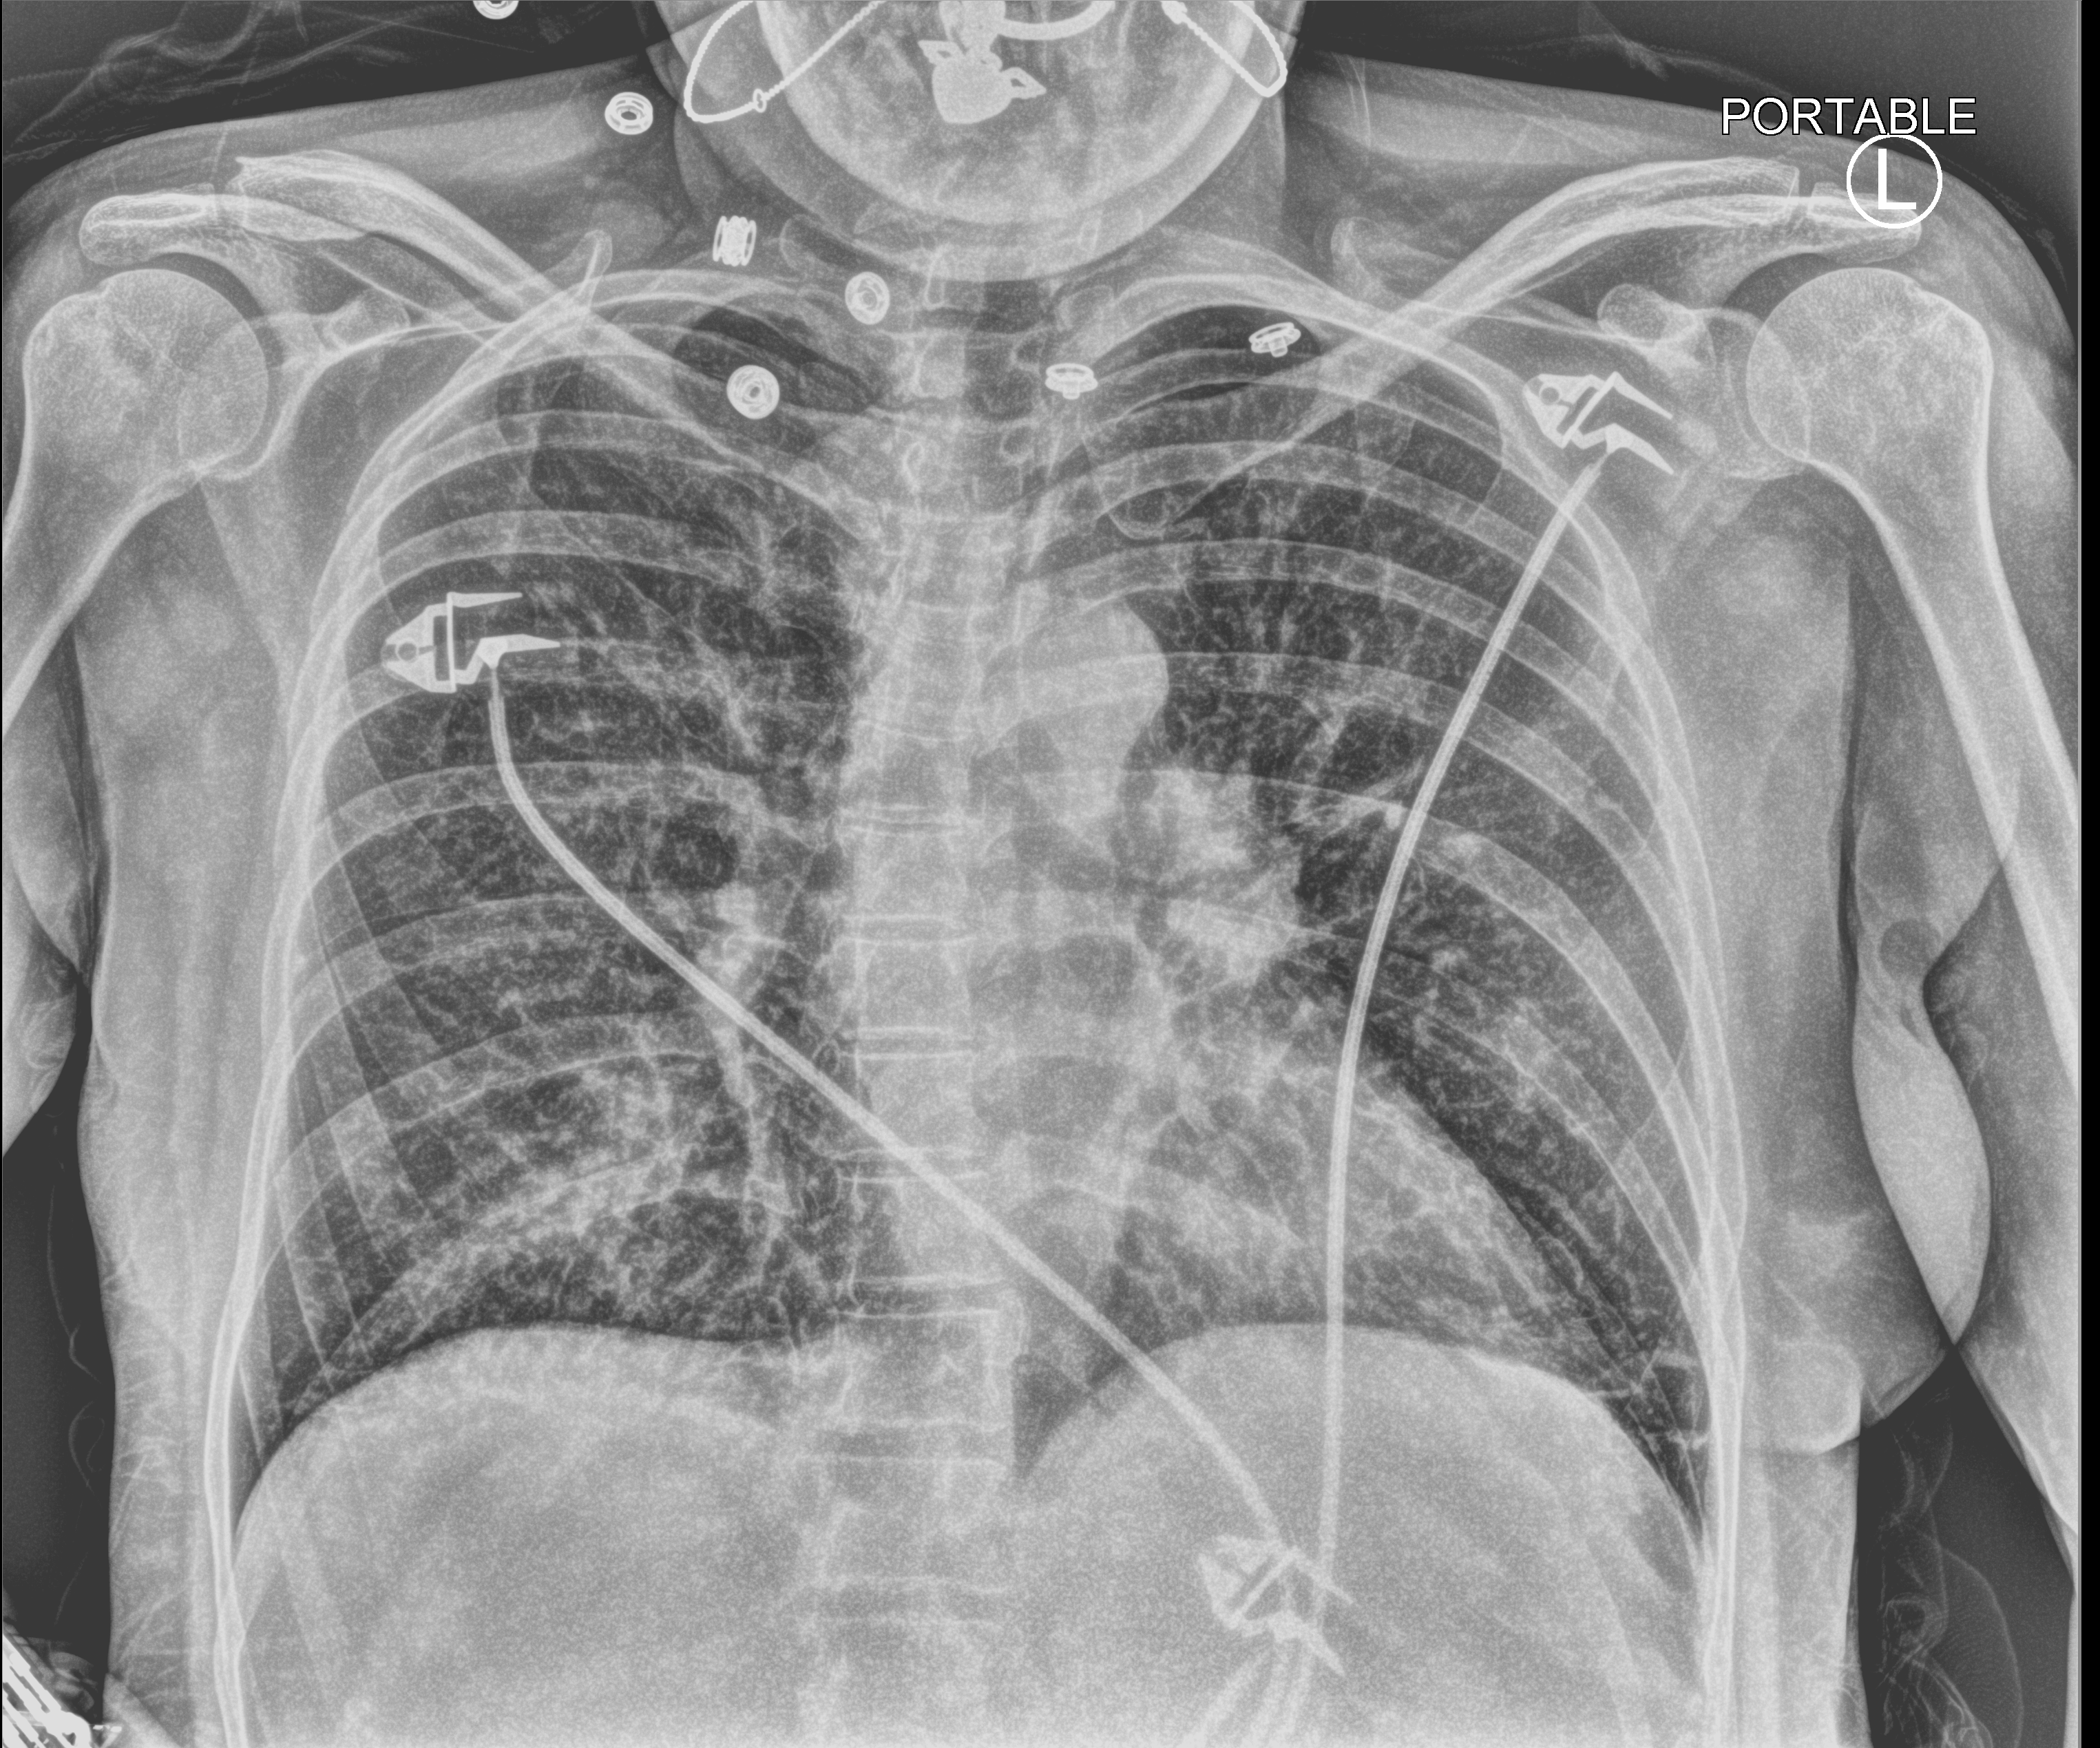
Bedside chest radiograph (computed radiography), anteroposterior (AP) projection. Patient hospitalised with COVID-19; female, aged 18–59 years.
From the hospital-stay record, not from the radiograph (when in the stay this image was taken is not recorded):
- COPD (admission record): no
- mechanically ventilated during this hospital stay: no